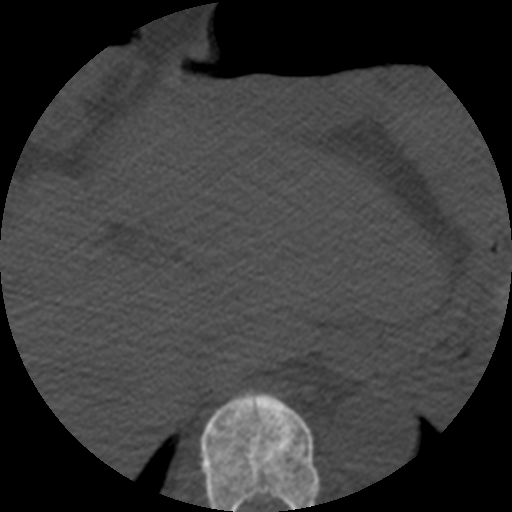
CT including the spine, one axial slice. Position 266 of 508 along the scan axis. Reconstruction kernel STANDARD. 120 kVp. Bone window (W 1800 / L 400 HU). 1.25 mm slice thickness. 512 × 512 image matrix, field of view 160 × 160 mm. Patient age 57 years. From the clinical record (not read from this slice): primary cancer: prostate.
Outlined on this slice (semi-automatically segmented with operator editing):
- T10 vertebra: box from (x=200, y=391) to (x=321, y=512) px